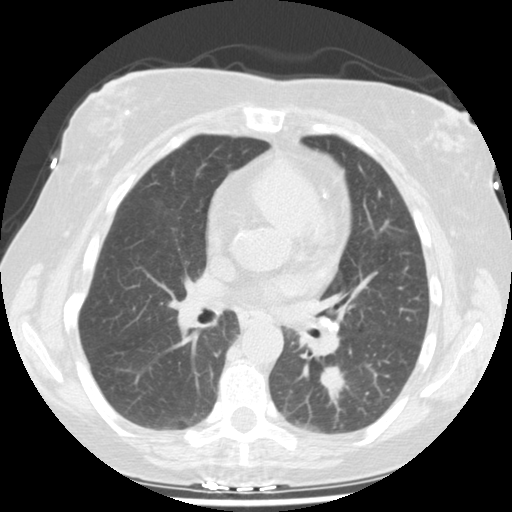
Low-dose screening chest CT, one axial slice. Position 93 of 159 along the scan axis. 120 kVp. Lung window (W 1500 / L -600 HU). 512 × 512 image matrix.
Structures marked on this image (manually delineated by an expert):
- lesion 1 (tumor, lower lobe of left lung): bounding box (x1, y1, x2, y2) in pixels: (320, 365, 348, 399)